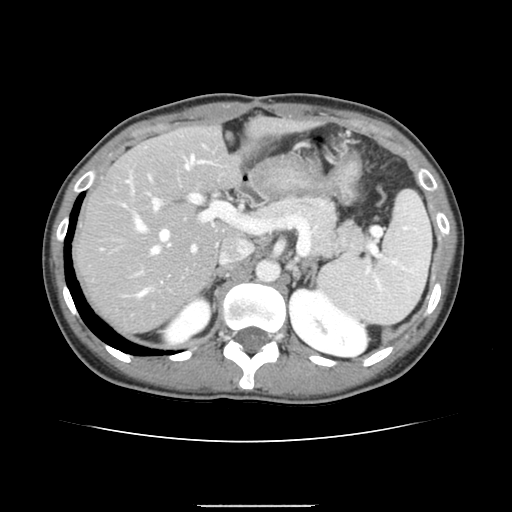
Contrast-enhanced abdominal CT, one axial slice; slice 96 of 150 in the series (ordered by position); 120 kVp; soft-tissue window (W 400 / L 40 HU); 512 × 512 image matrix, field of view 324 × 324 mm. Female patient, age 32 years. From the clinical record (not read from this slice): diagnosis: colorectal cancer liver metastases, imaged before liver resection; multiple liver metastases: yes; largest metastasis: 0.7 cm; disease in both lobes: no.
Outlined on this slice (expert manual segmentation):
- hepatic veins: box from (x=135, y=156) to (x=203, y=296) px
- liver: (x=76, y=123)–(x=296, y=332)
- planned liver remnant (the part of the liver to remain after resection): (x=76, y=123)–(x=296, y=280)
- portal vein (with intrahepatic branches): (x=123, y=176)–(x=233, y=274)